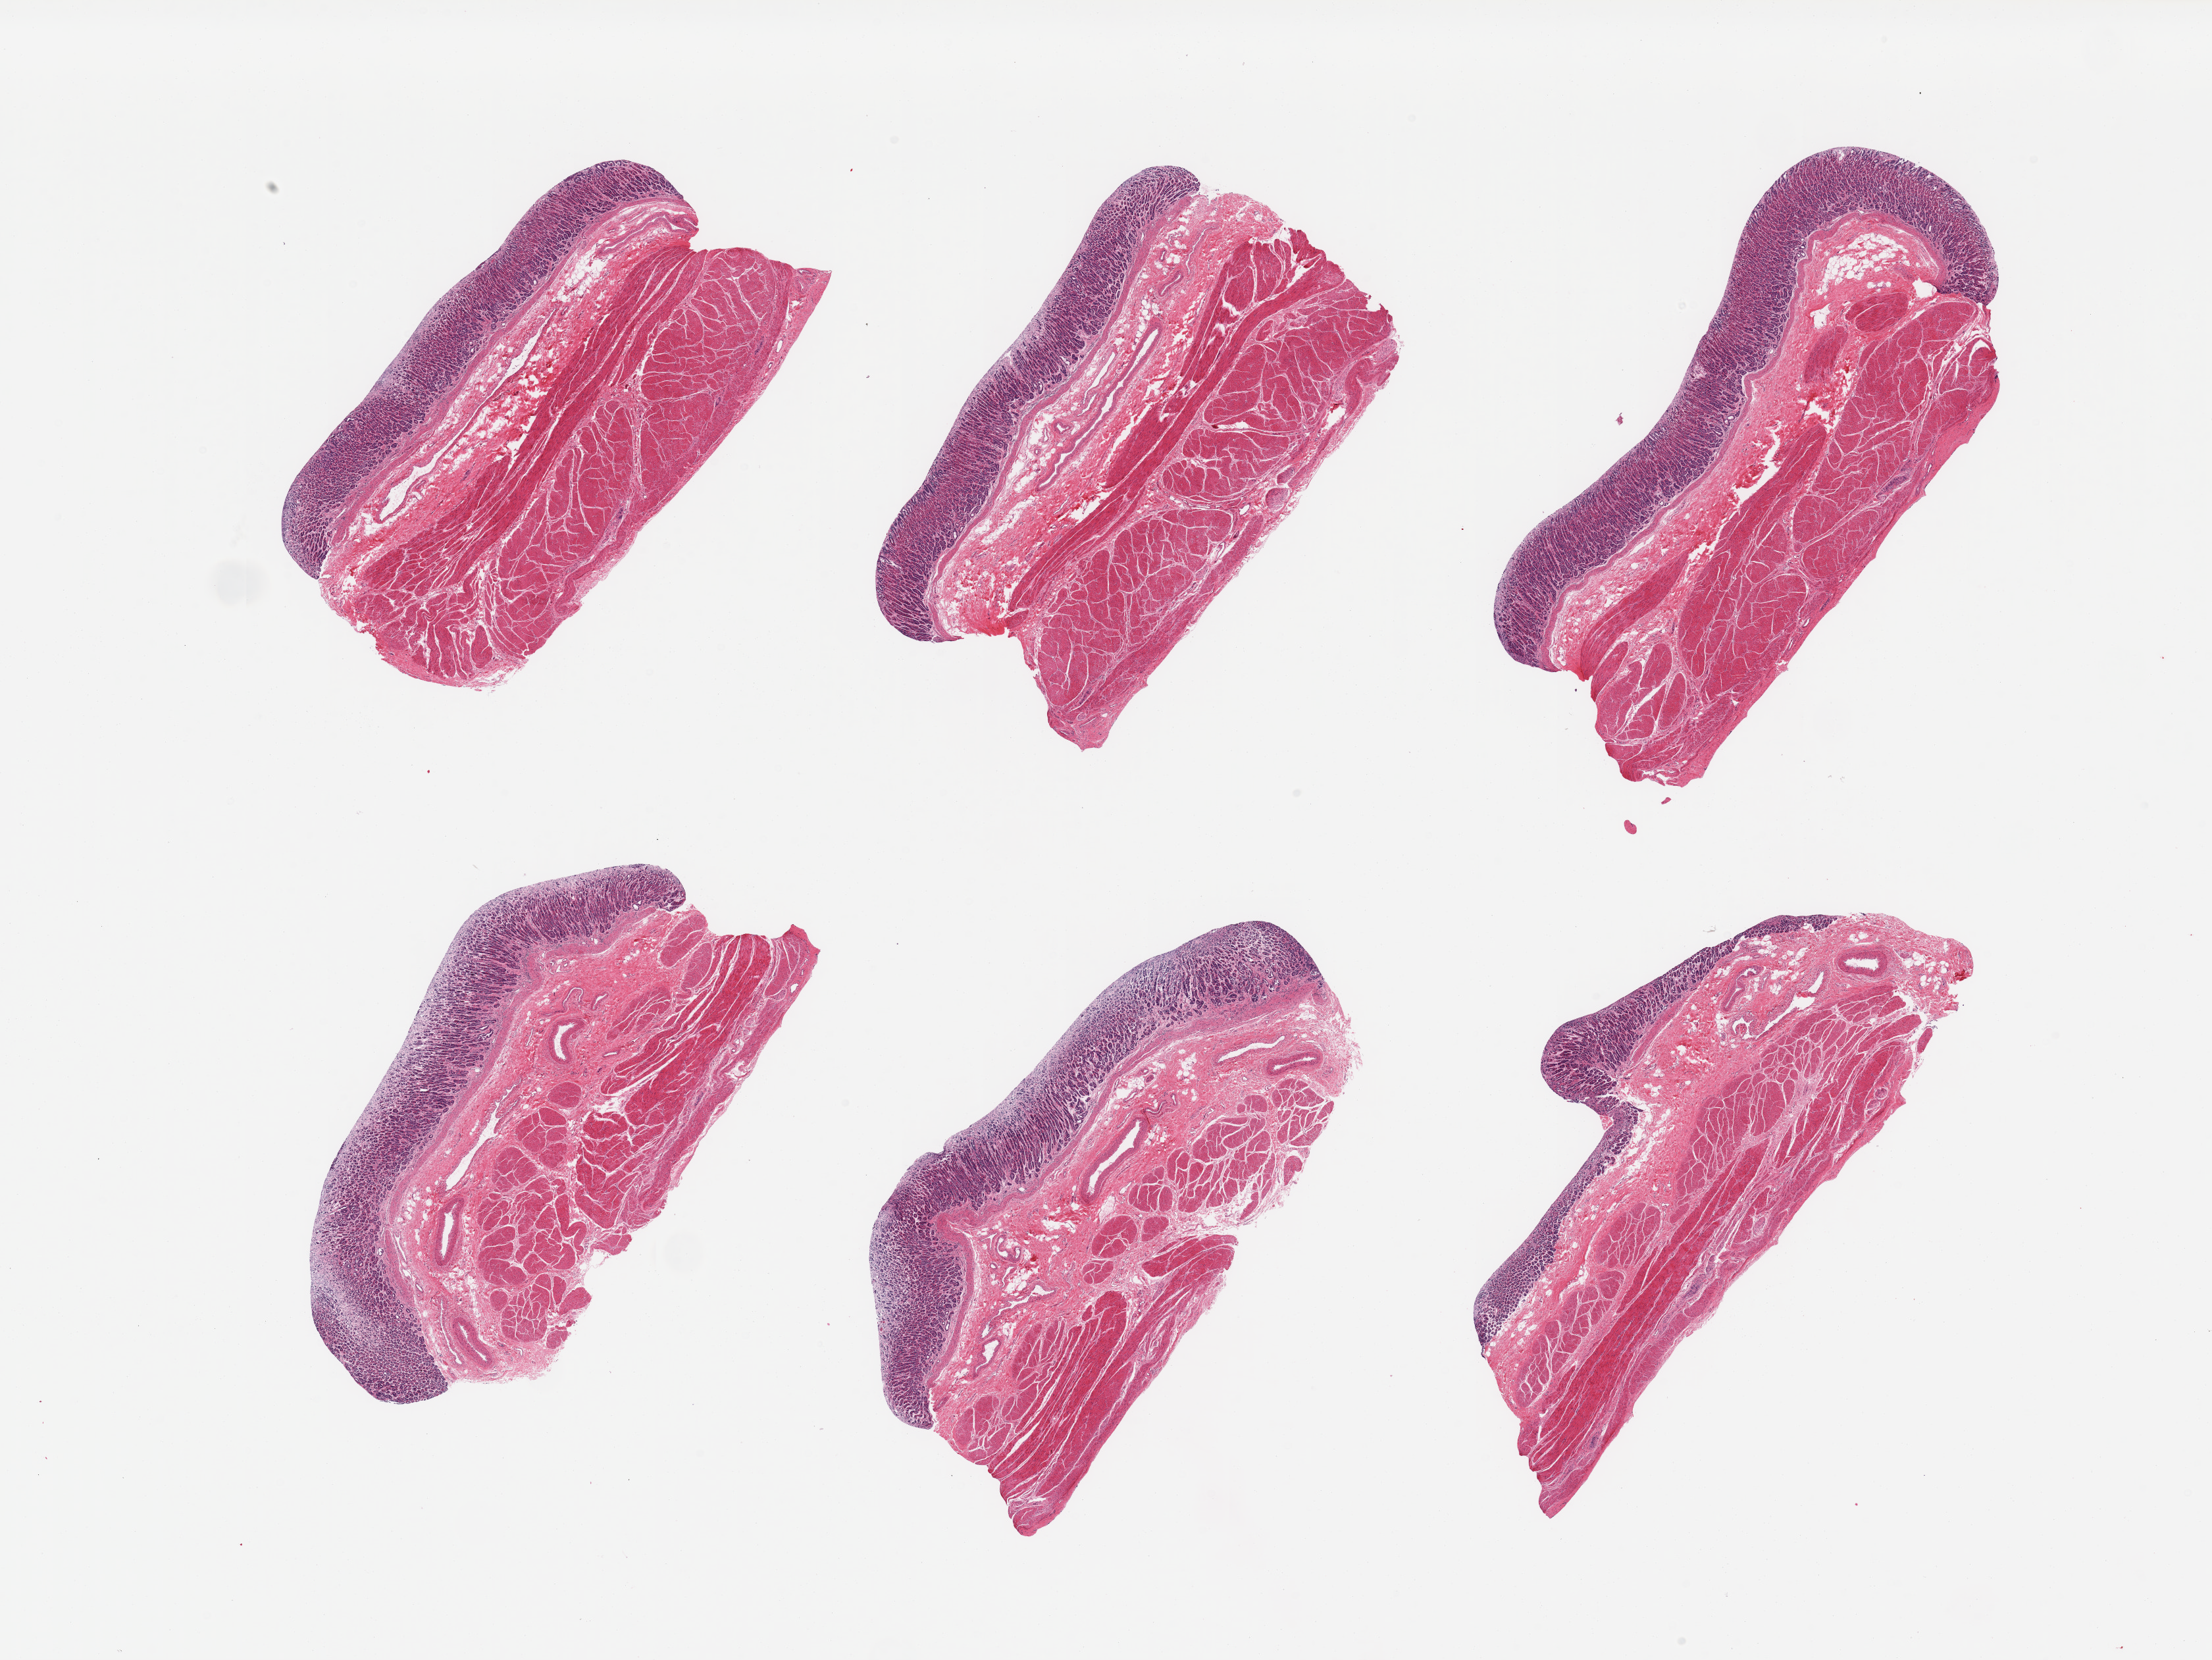
Digitized H&E-stained section, brightfield, a low-resolution overview of the entire scanned area, about 26.6 x 19.9 mm; PAXgene-fixed, paraffin-embedded tissue; target tissue: stomach; tissue donor sample. Male donor.
• reviewer comment on this tissue sample: 6 pieces; mucosa ranges from slight to moderate autolysis; muscularis has slight autolysis